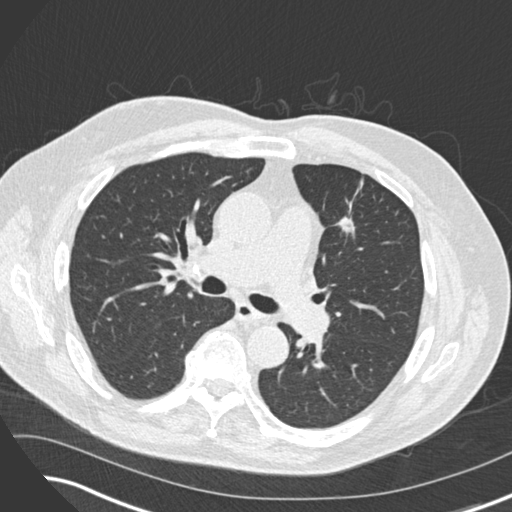
Axial slice from a low-dose chest CT screening exam; third screening round (two years after baseline); lung window (W 1500 / L -600 HU). Male participant, aged 74 years at enrolment. Former smoker at enrolment.
• Expert-annotated lung lesion, bounding box [x1, y1, x2, y2] px = [319, 197, 375, 247].
• The exam's reader record, not a measurement of the box and not confirmed to be the same lesion: non-calcified nodule or mass ≥4 mm, left upper lobe, 12 × 10 mm, spiculated (stellate) margins, soft tissue attenuation, pre-existing on the prior screen: yes; interval growth: yes.